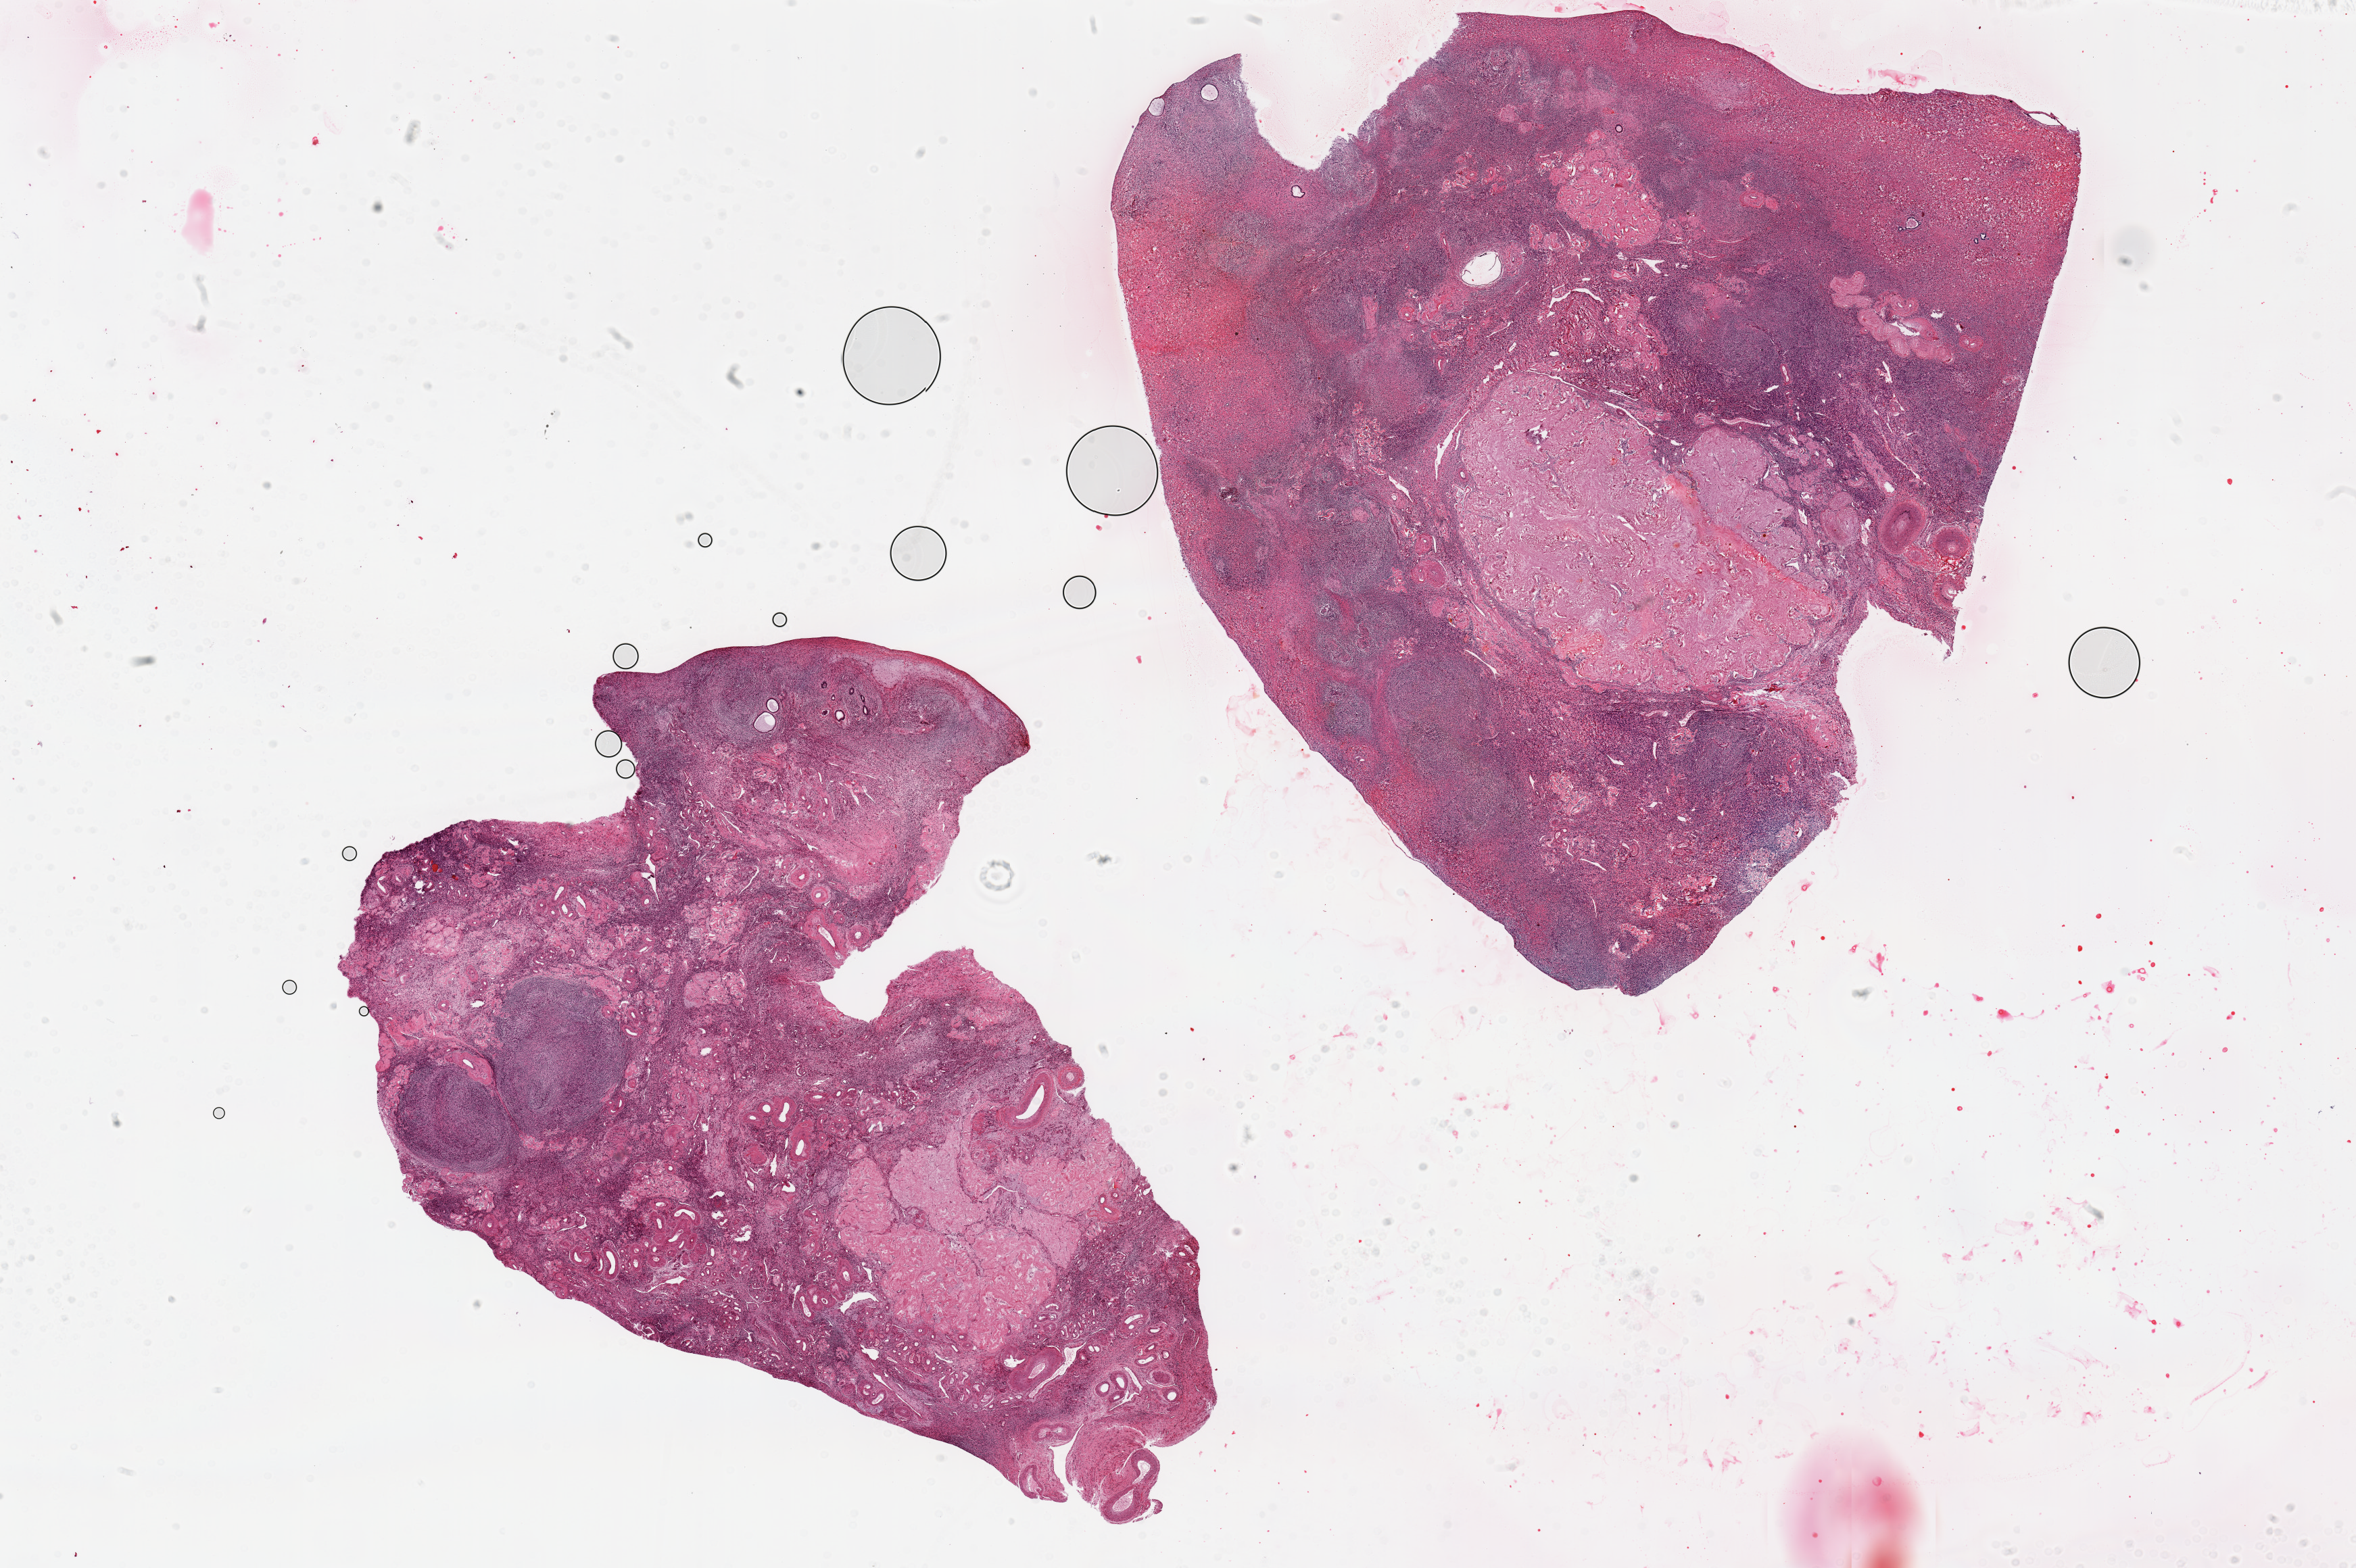
Whole-slide image, haematoxylin and eosin stain, shown as a low-resolution overview of the whole scanned area (about 27.6 x 18.3 mm), PAXgene-fixed, paraffin-embedded tissue, section of ovary (target tissue), tissue donor sample. Donor sex: female.
Pathologist's review note for this sample: 2 pieces, 12x9 & 12x11mm; numerous c. albicans, some follicles.